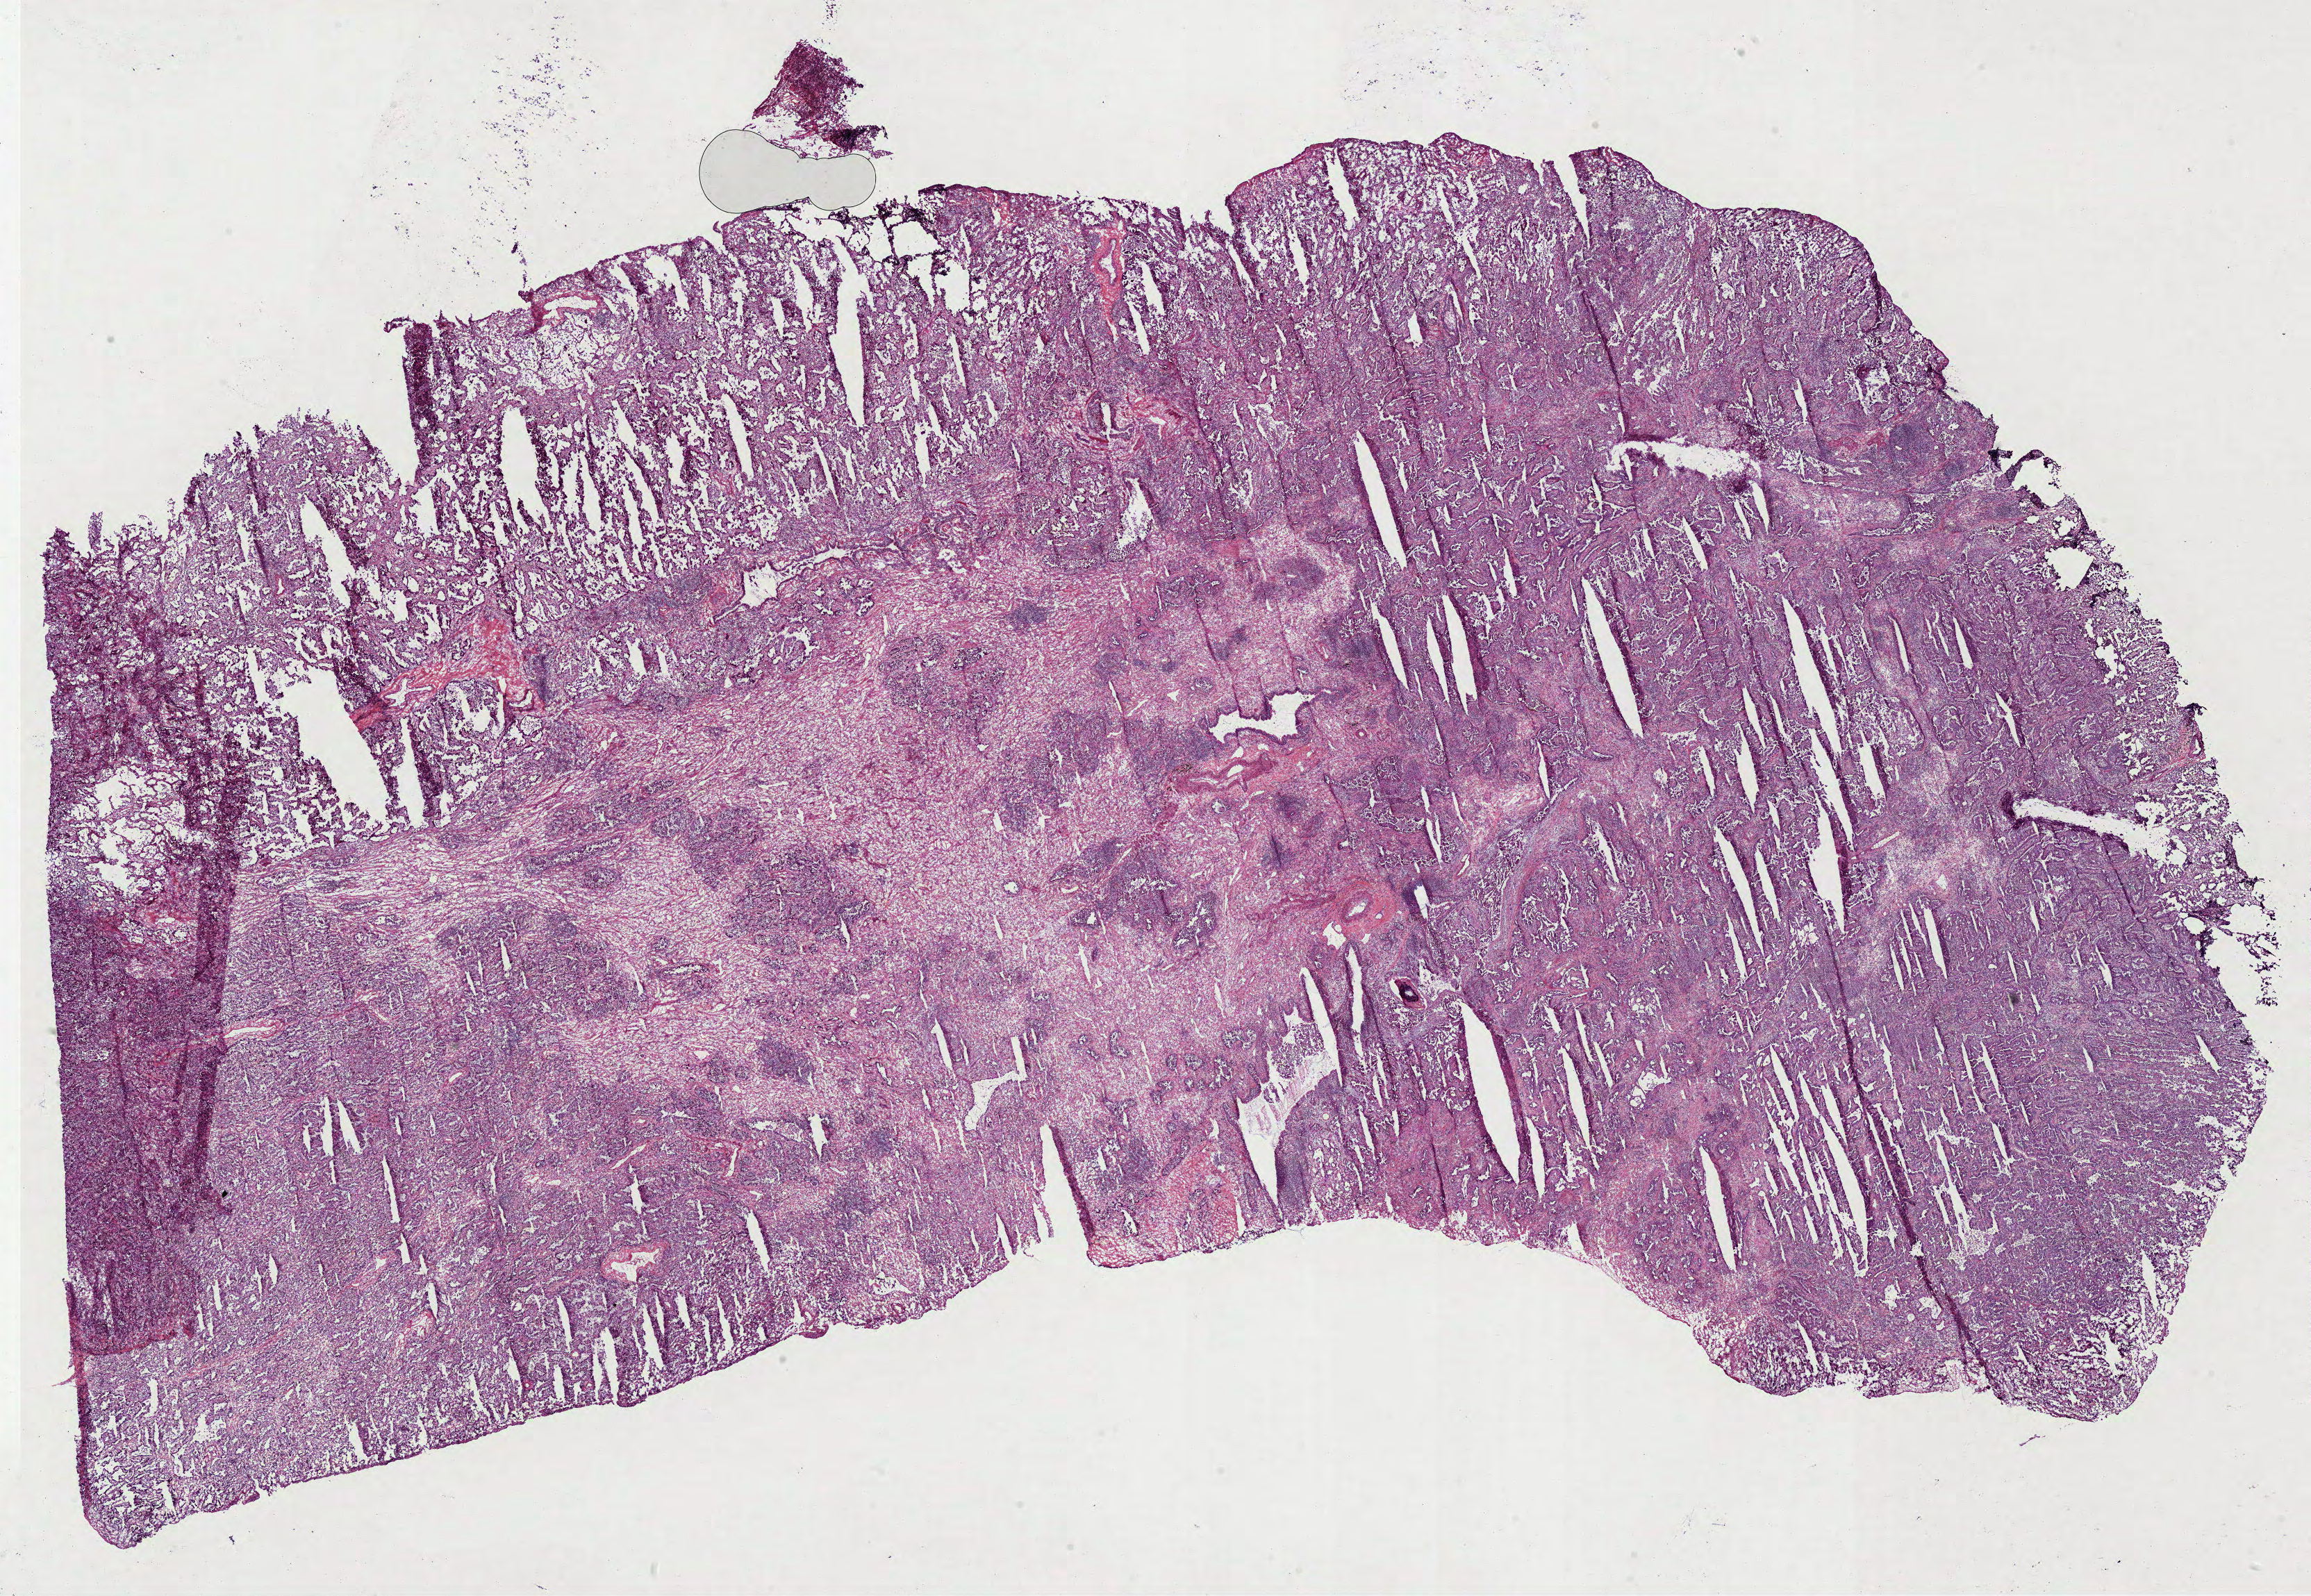
Digitized H&E-stained tissue section (whole slide), a low-resolution overview of the entire scanned area, about 26.8 x 18.5 mm. Frozen section from the top of the tissue portion. Sample: primary tumour, lung. Patient: female, age at initial diagnosis 54 years. Slide review estimates, as recorded: tumour cells 80%, tumour nuclei 70%, normal cells 0%, stromal cells 20%, necrosis 0%.
Histologic diagnosis: Bronchiolo-alveolar carcinoma, non-mucinous (lower lobe, lung). AJCC pathologic stage: IIA.